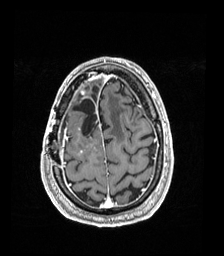
Brain MRI from a brain-tumour surgery series, one axial slice; position 41 of 192 along the scan axis; T1-weighted post-contrast; 1 mm slice thickness; 224 × 256 image matrix, field of view 224 × 256 mm. Case-level facts recorded for this patient, not image findings: histopathology: Astrocytoma; WHO grade: 4; IDH mutation: yes; tumour location: Right Frontal.
Outlined on this slice (outlined manually by an expert reader):
- previous resection cavity: bounding box (x1, y1, x2, y2) in pixels: (73, 99, 97, 137)
- tumour: (80, 90, 85, 154)